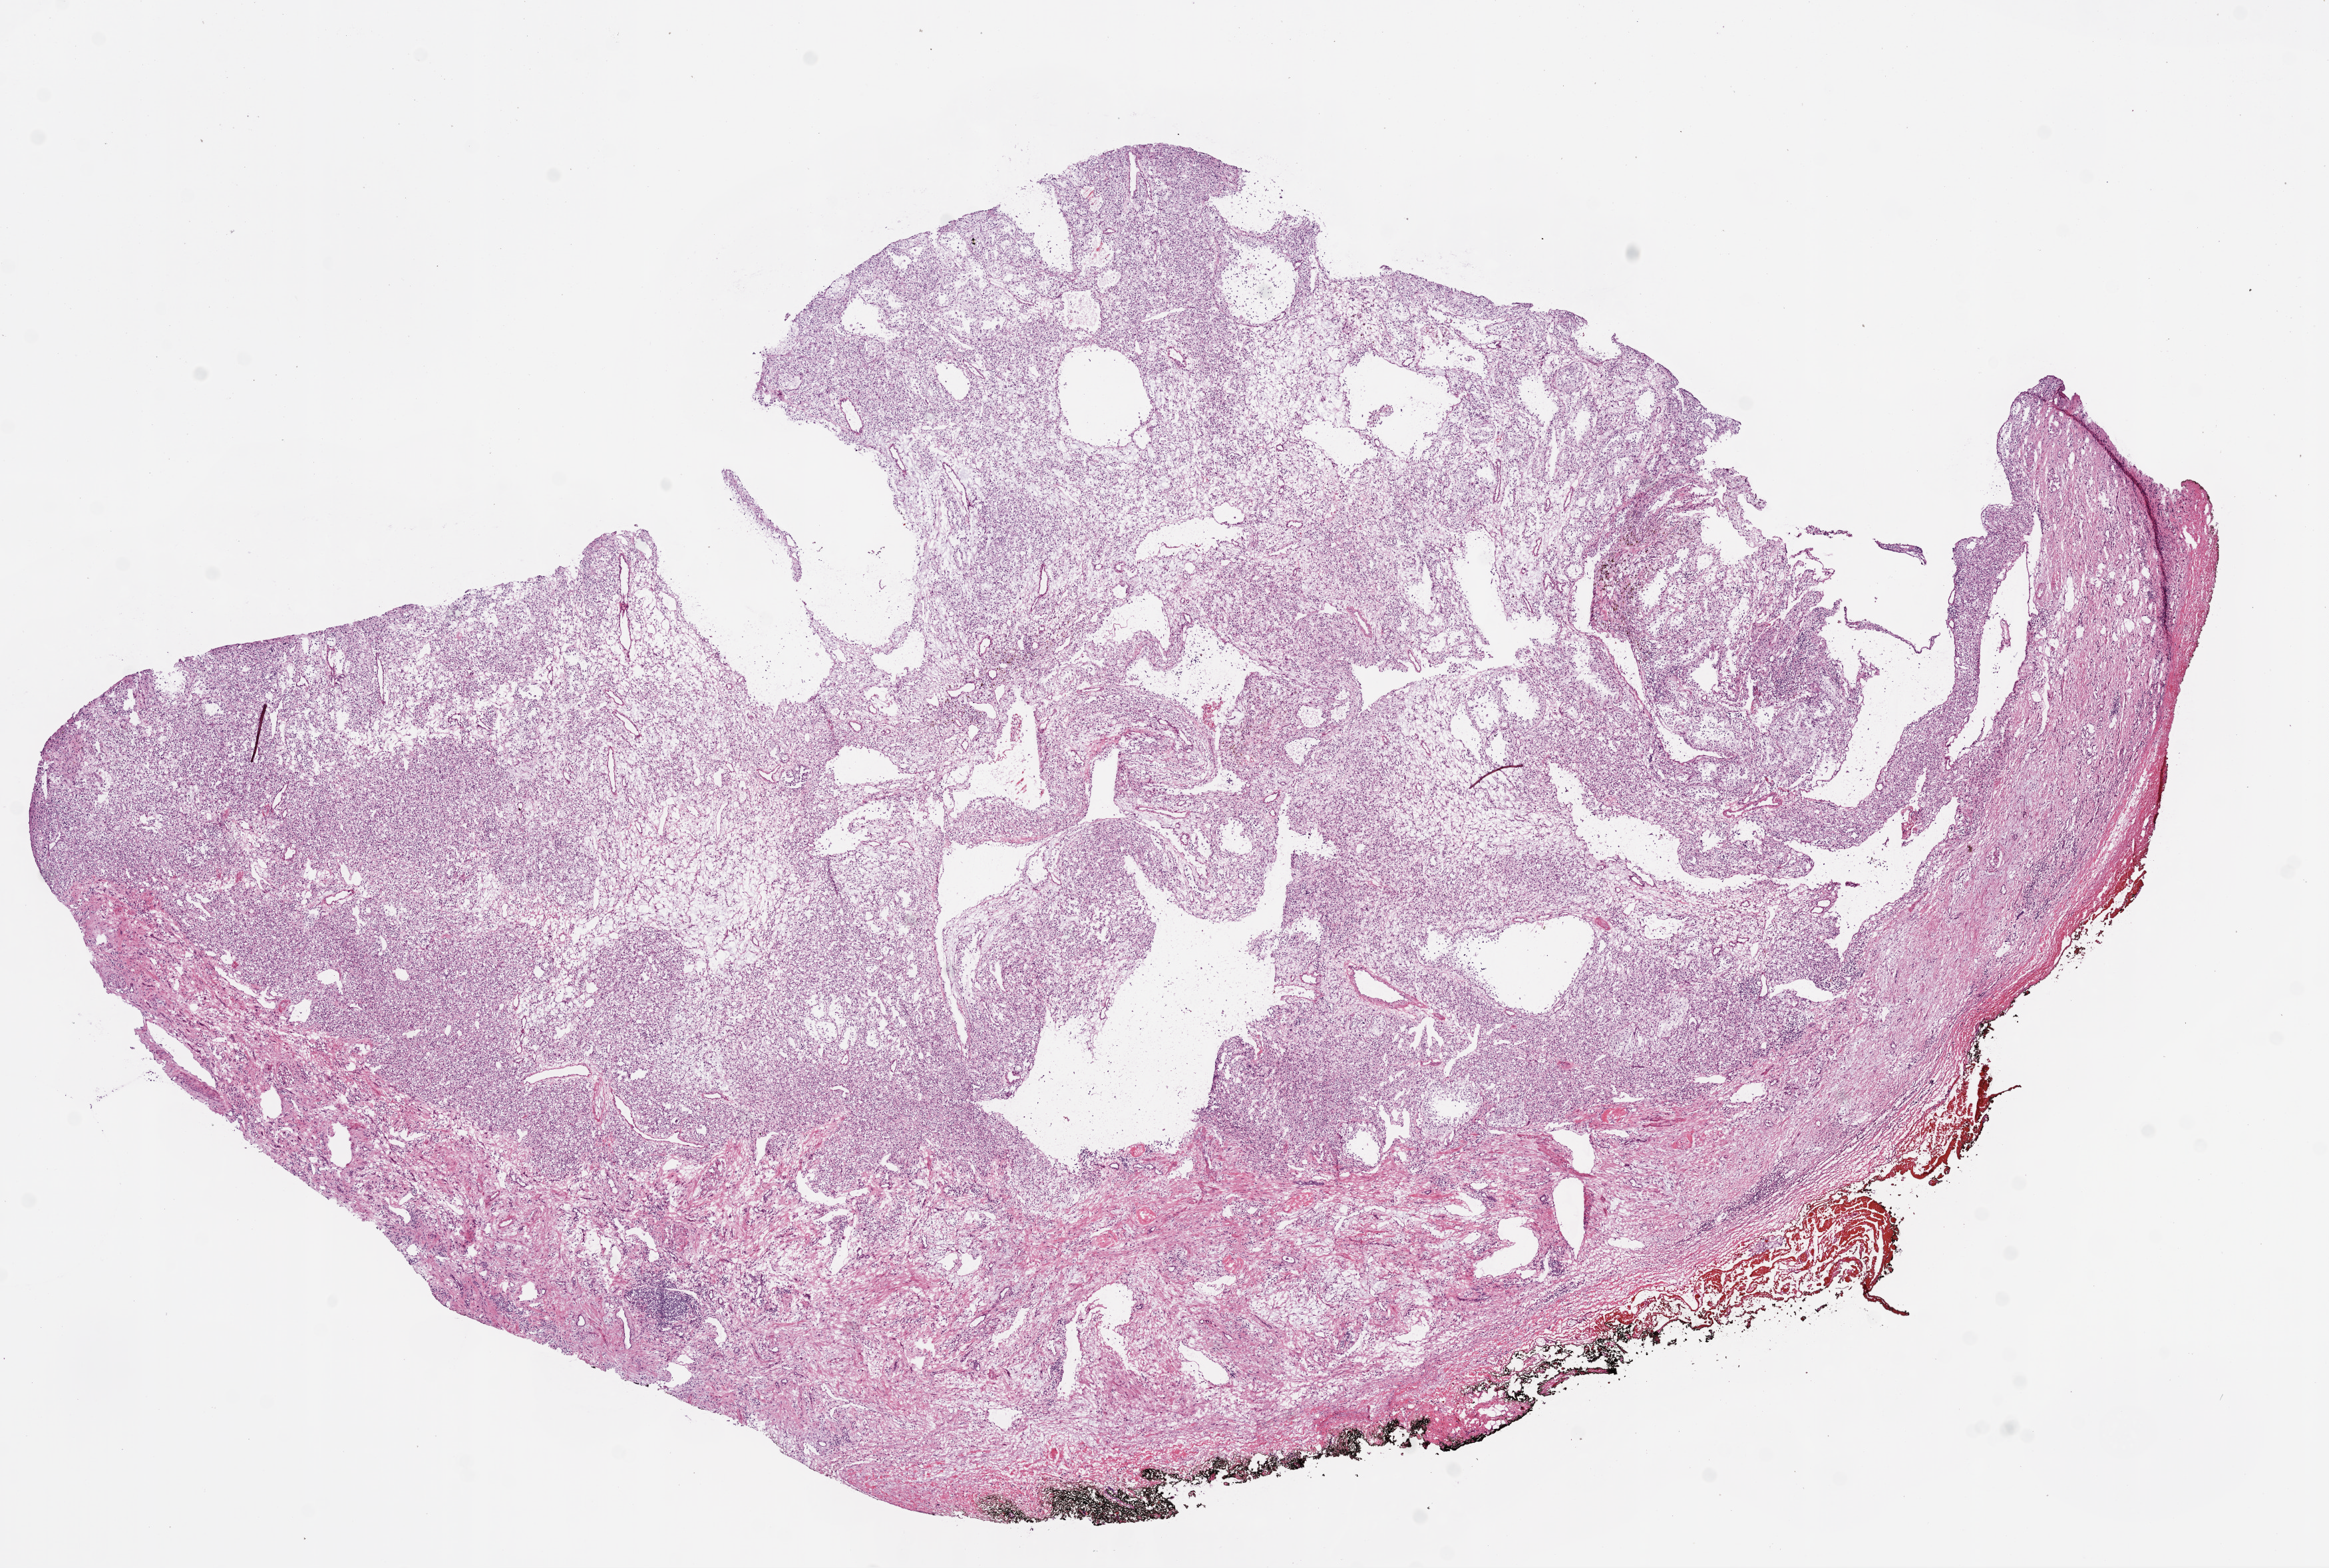
Digitized Hematoxylin and eosin (H&E) stained tissue section (whole slide), low-resolution overview of the scanned area, about 14.0 x 9.5 mm (acquisition: 20x scan). Frozen section. Primary tumour sample from the kidney. Male patient; age at initial diagnosis 42 years.
Diagnosis: Clear cell adenocarcinoma, NOS.